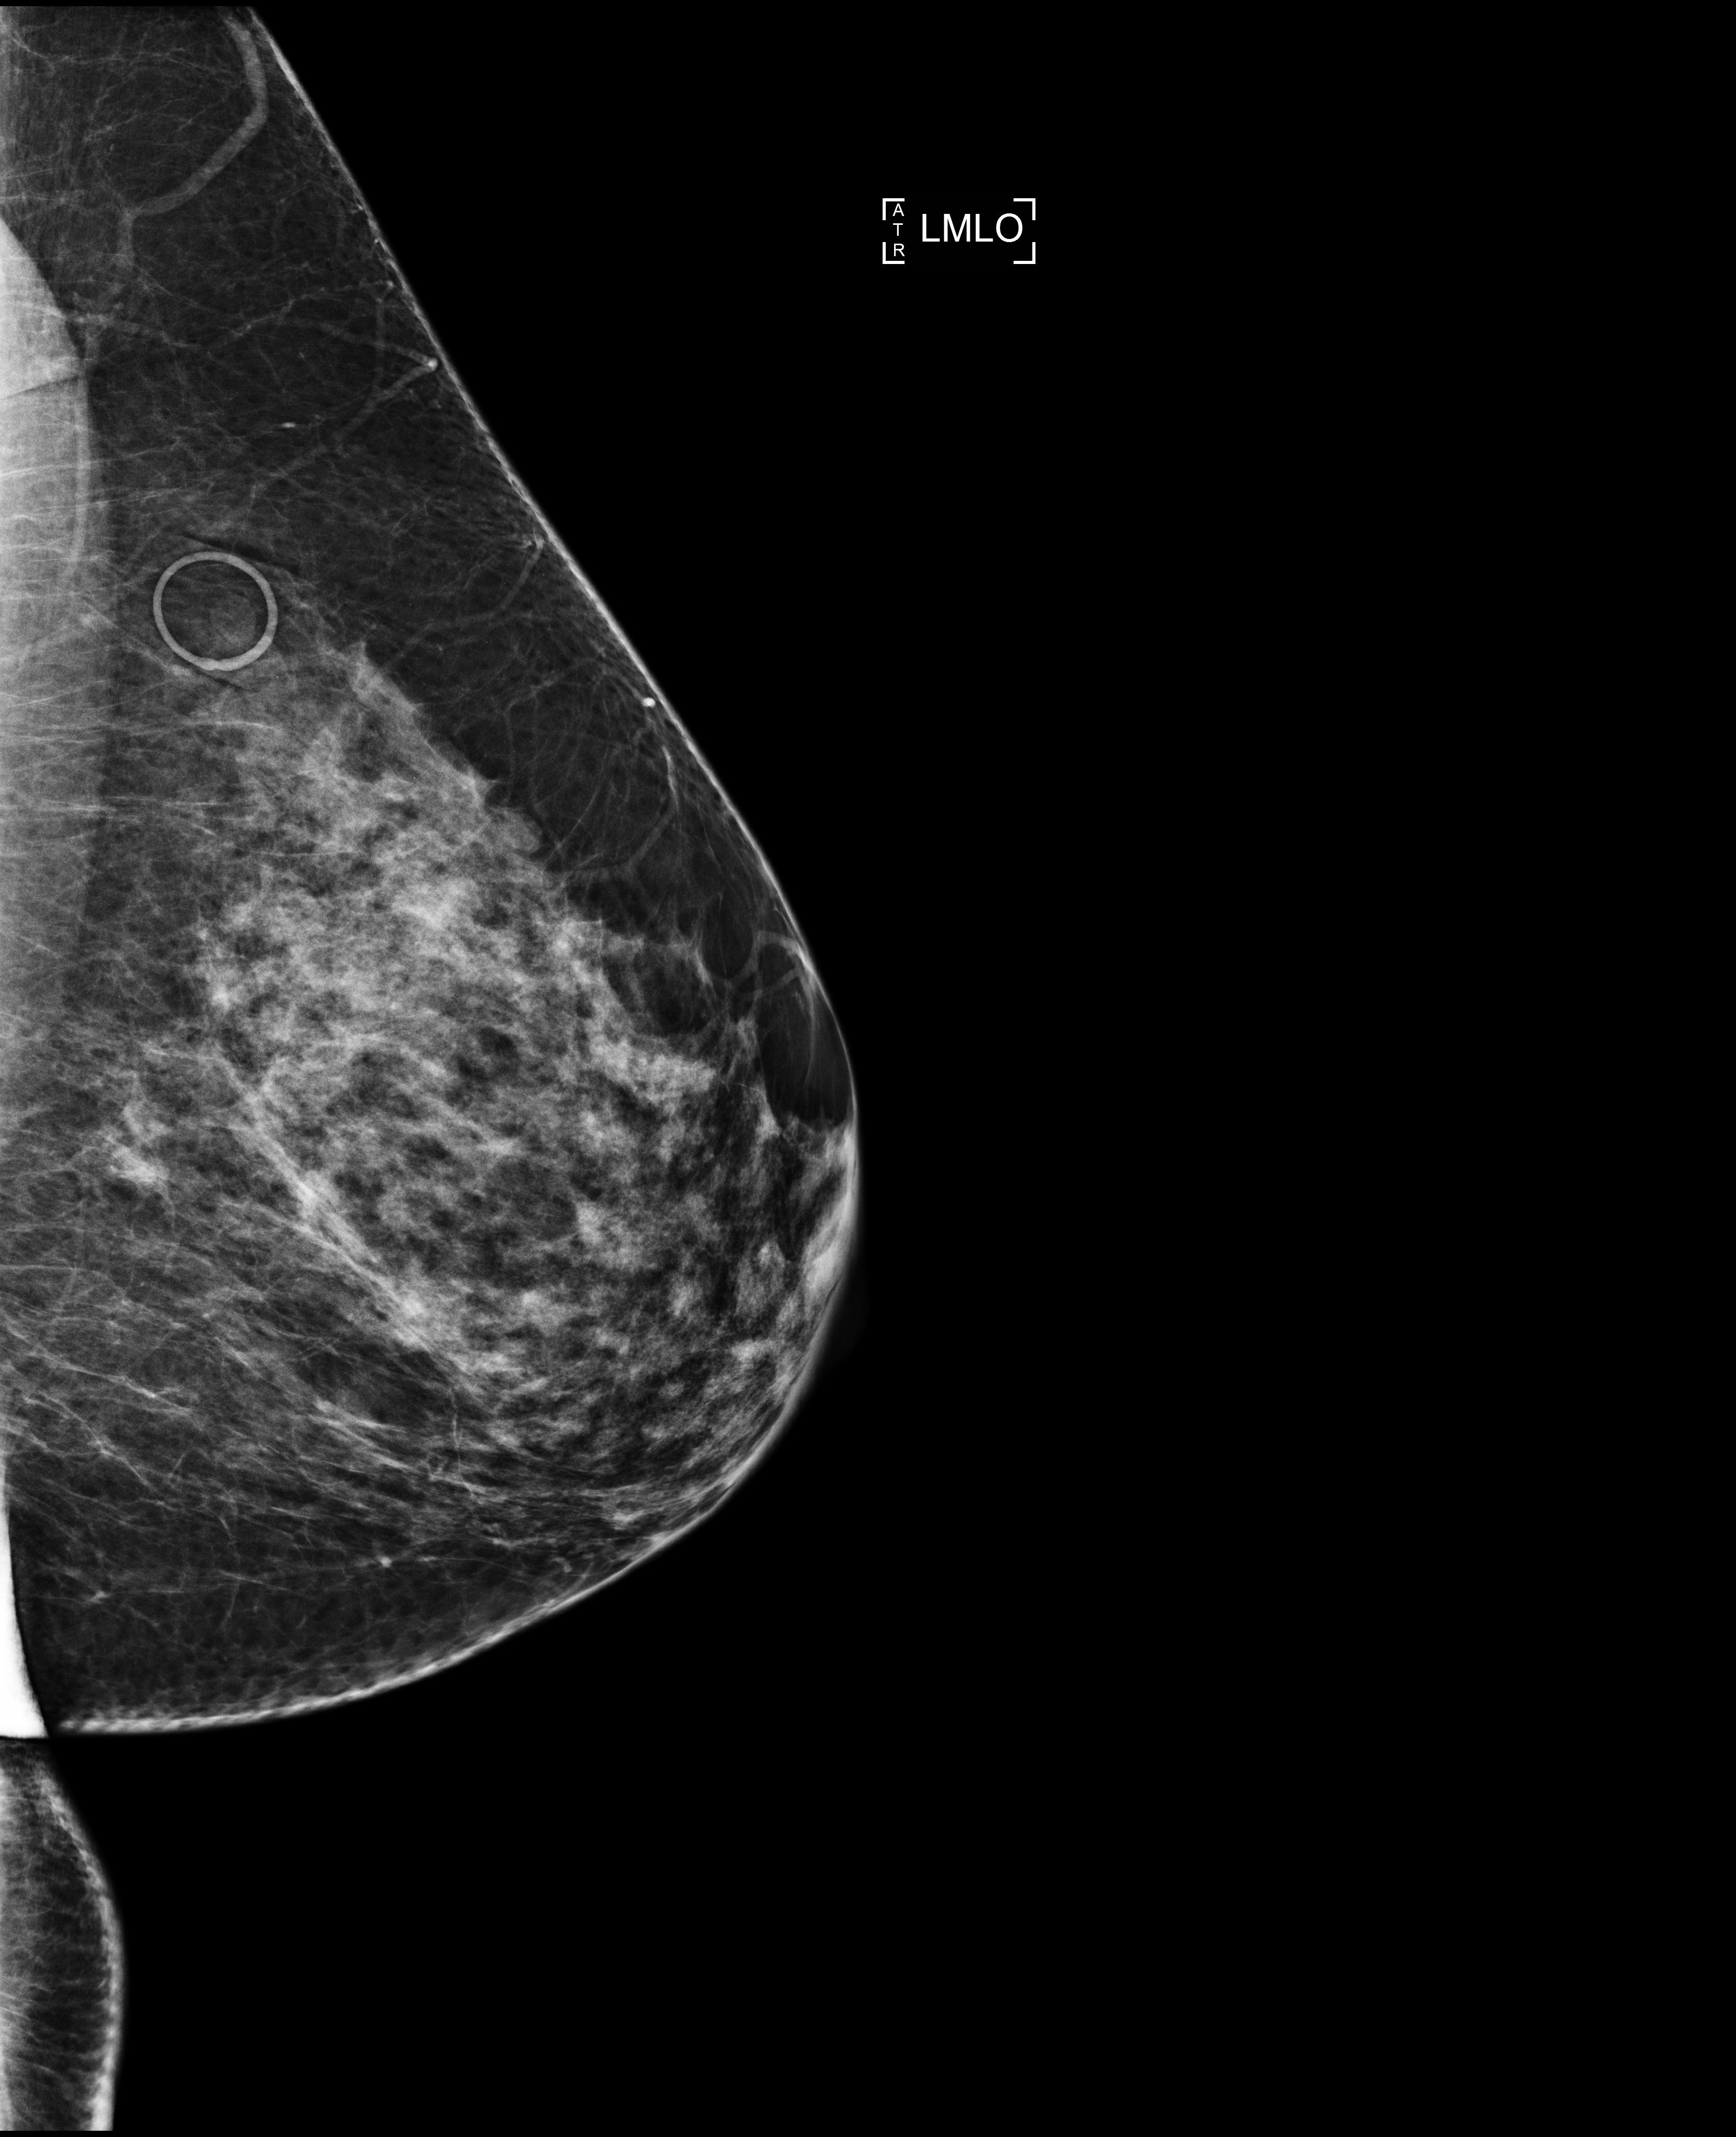
Screening examination; system: Selenia Dimensions. Patient aged 53 years (female).
Image type: full-field digital mammogram. Breast: left. Projection: medio-lateral oblique projection.